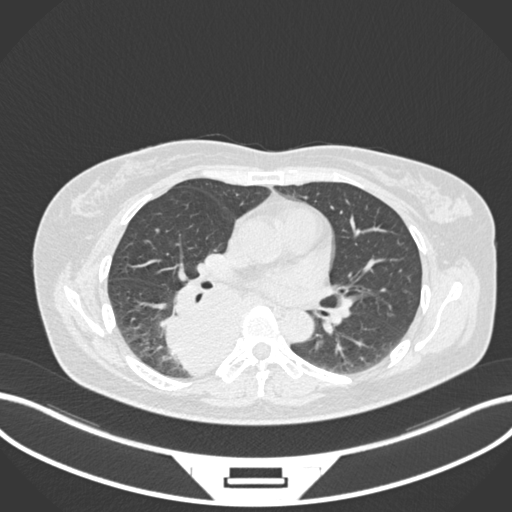
Chest CT, one axial slice. Slice 592 of 677 in the series (ordered by position). Lung window (W 1500 / L -600 HU). 512 × 512 image matrix. Female patient, age 54 years. From the clinical record (not read from this slice): clinical TNM (as recorded): T4 N0 M0.
Annotated regions visible in this slice (bounding box drawn by a radiologist):
- lung tumour (recorded histology: adenocarcinoma): bounding box (x1, y1, x2, y2) in pixels: (158, 280, 250, 378)